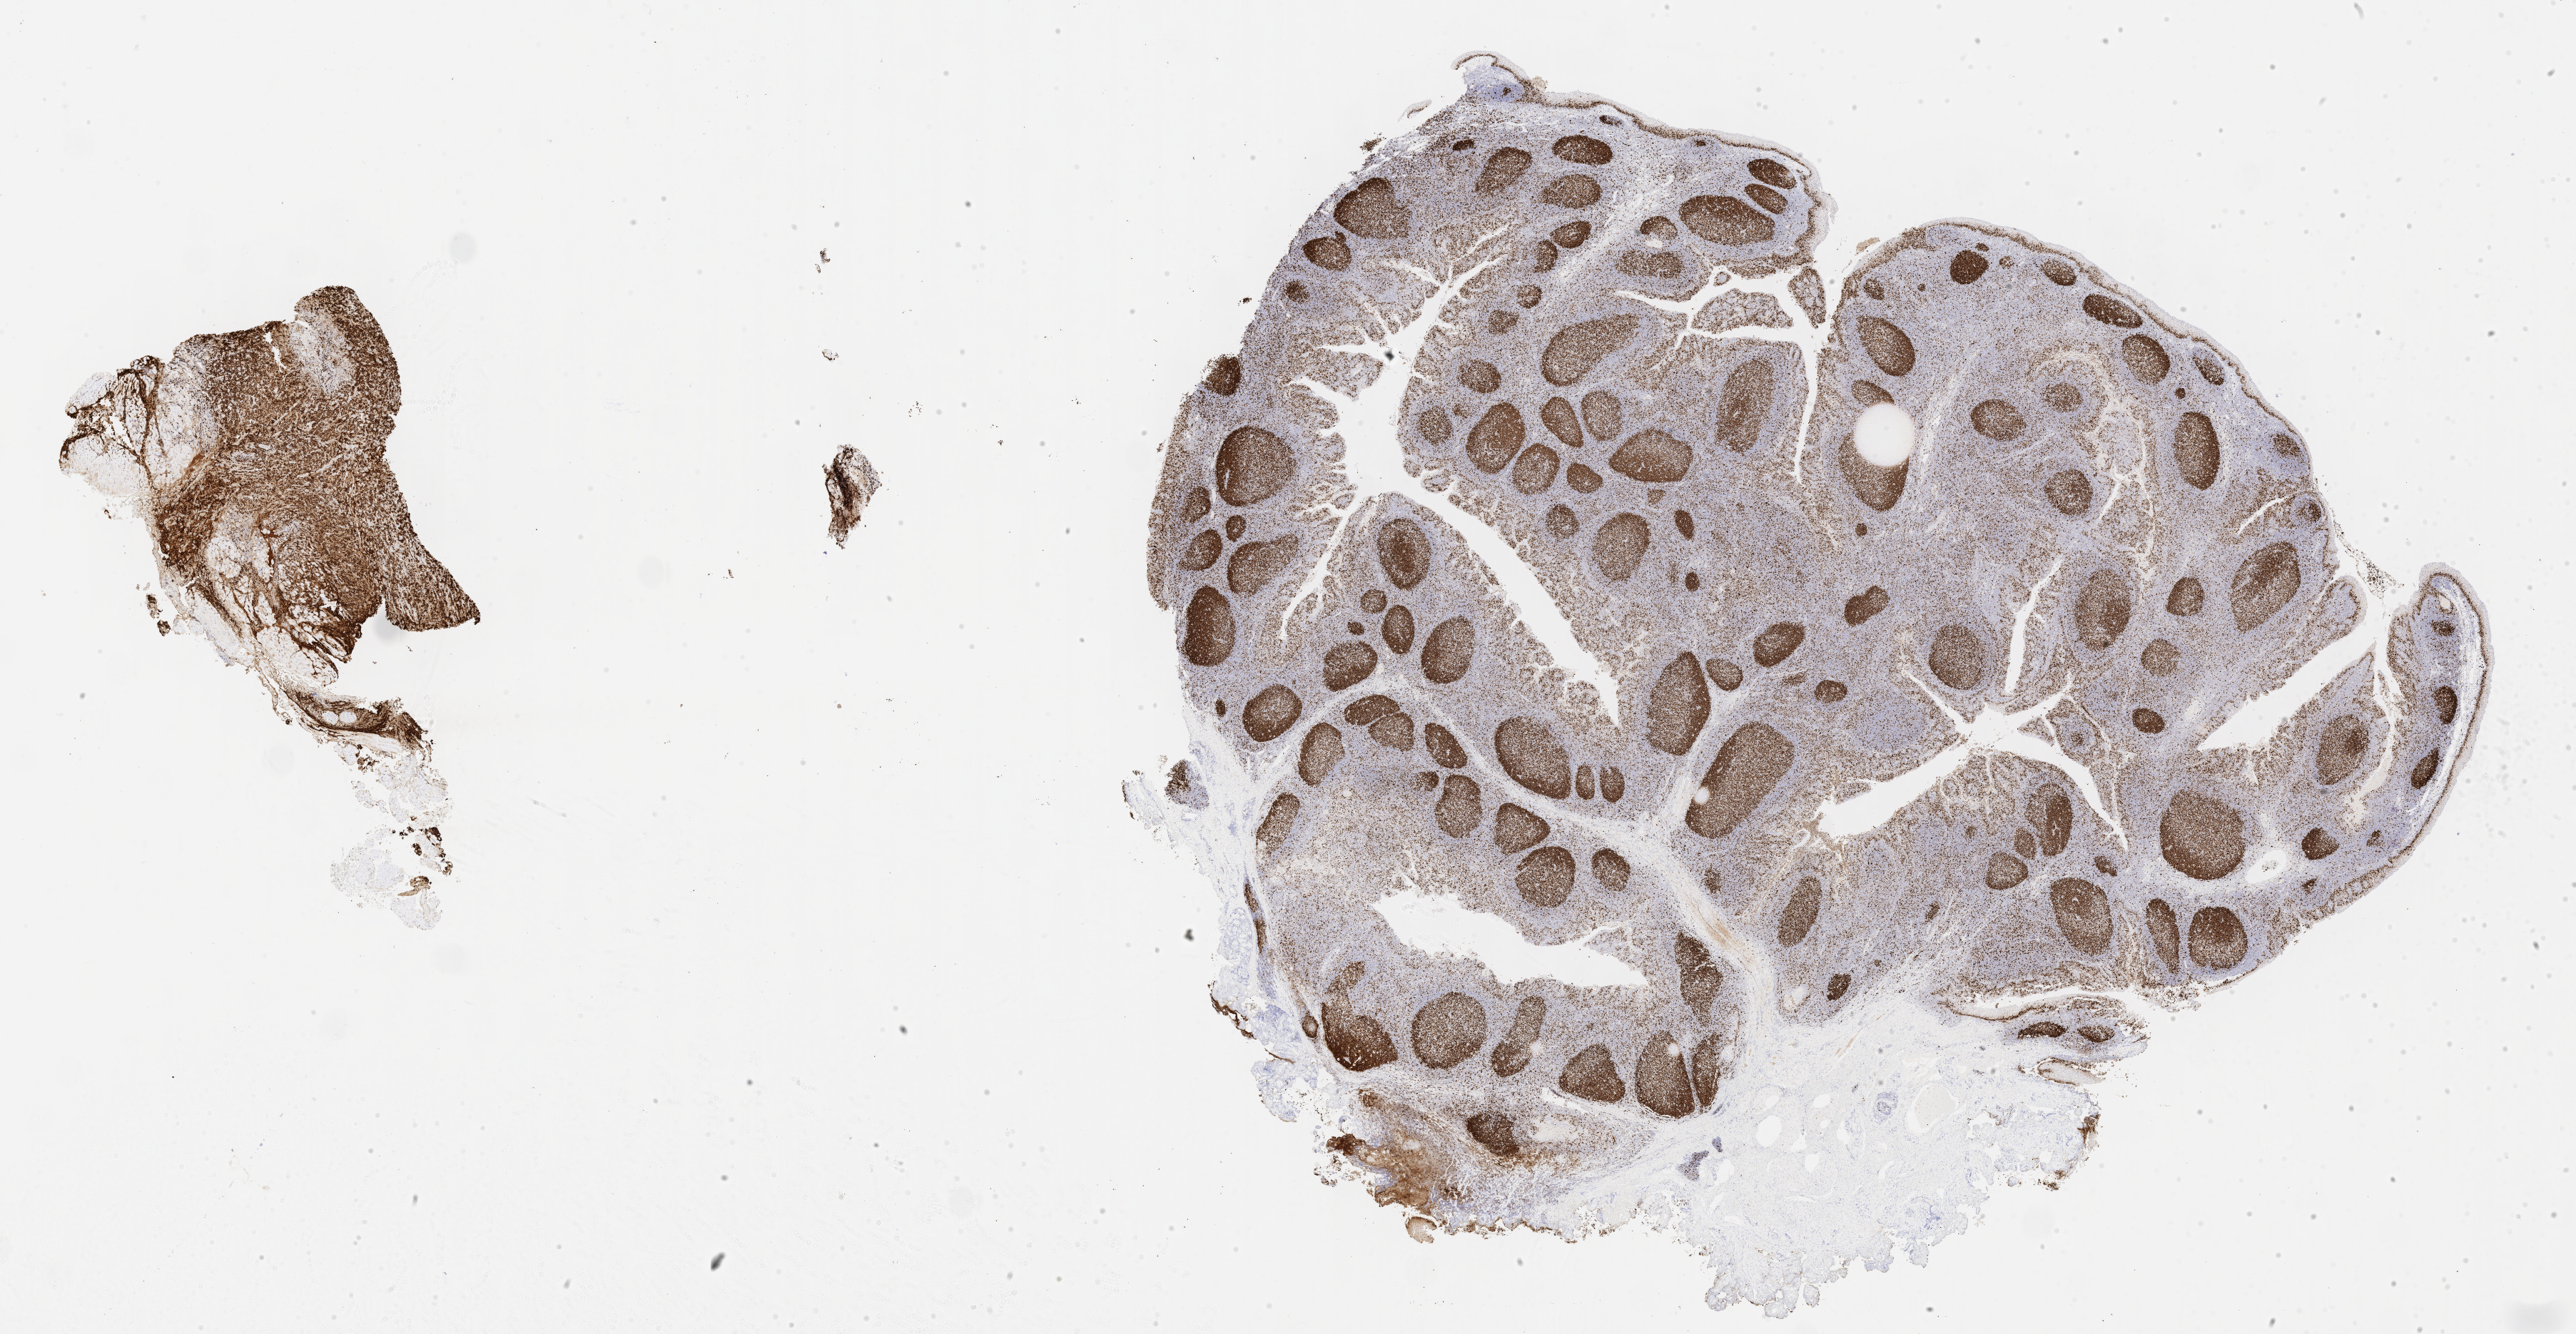
Whole-slide image, immunohistochemical stain for Ki-67 — whole scanned area (about 29.2 x 15.1 mm) shown as a low-resolution overview. Specimen: tumor tissue. Anatomic site: kidney. Male patient, 12 years old.
- histologic diagnosis: Diffuse large B-cell lymphoma, NOS